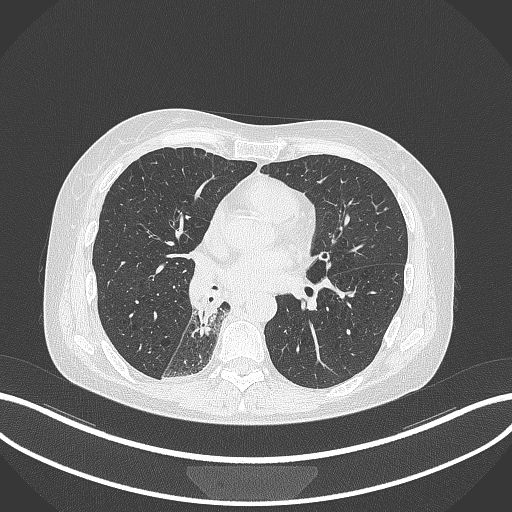
Chest CT, one axial slice; position 145 of 329 along the scan axis; reconstruction kernel B70f; lung window (W 1500 / L -600 HU); 1 mm slice thickness; 512 × 512 image matrix. Patient: female, 63 years. Case-level facts recorded for this patient, not image findings: clinical TNM (as recorded): T1c N0 M0.
Outlined on this slice (rectangle marked by the reading radiologist):
- lung tumour (recorded histology: adenocarcinoma): bounding box <194,284,224,338> (left, top, right, bottom; pixels)